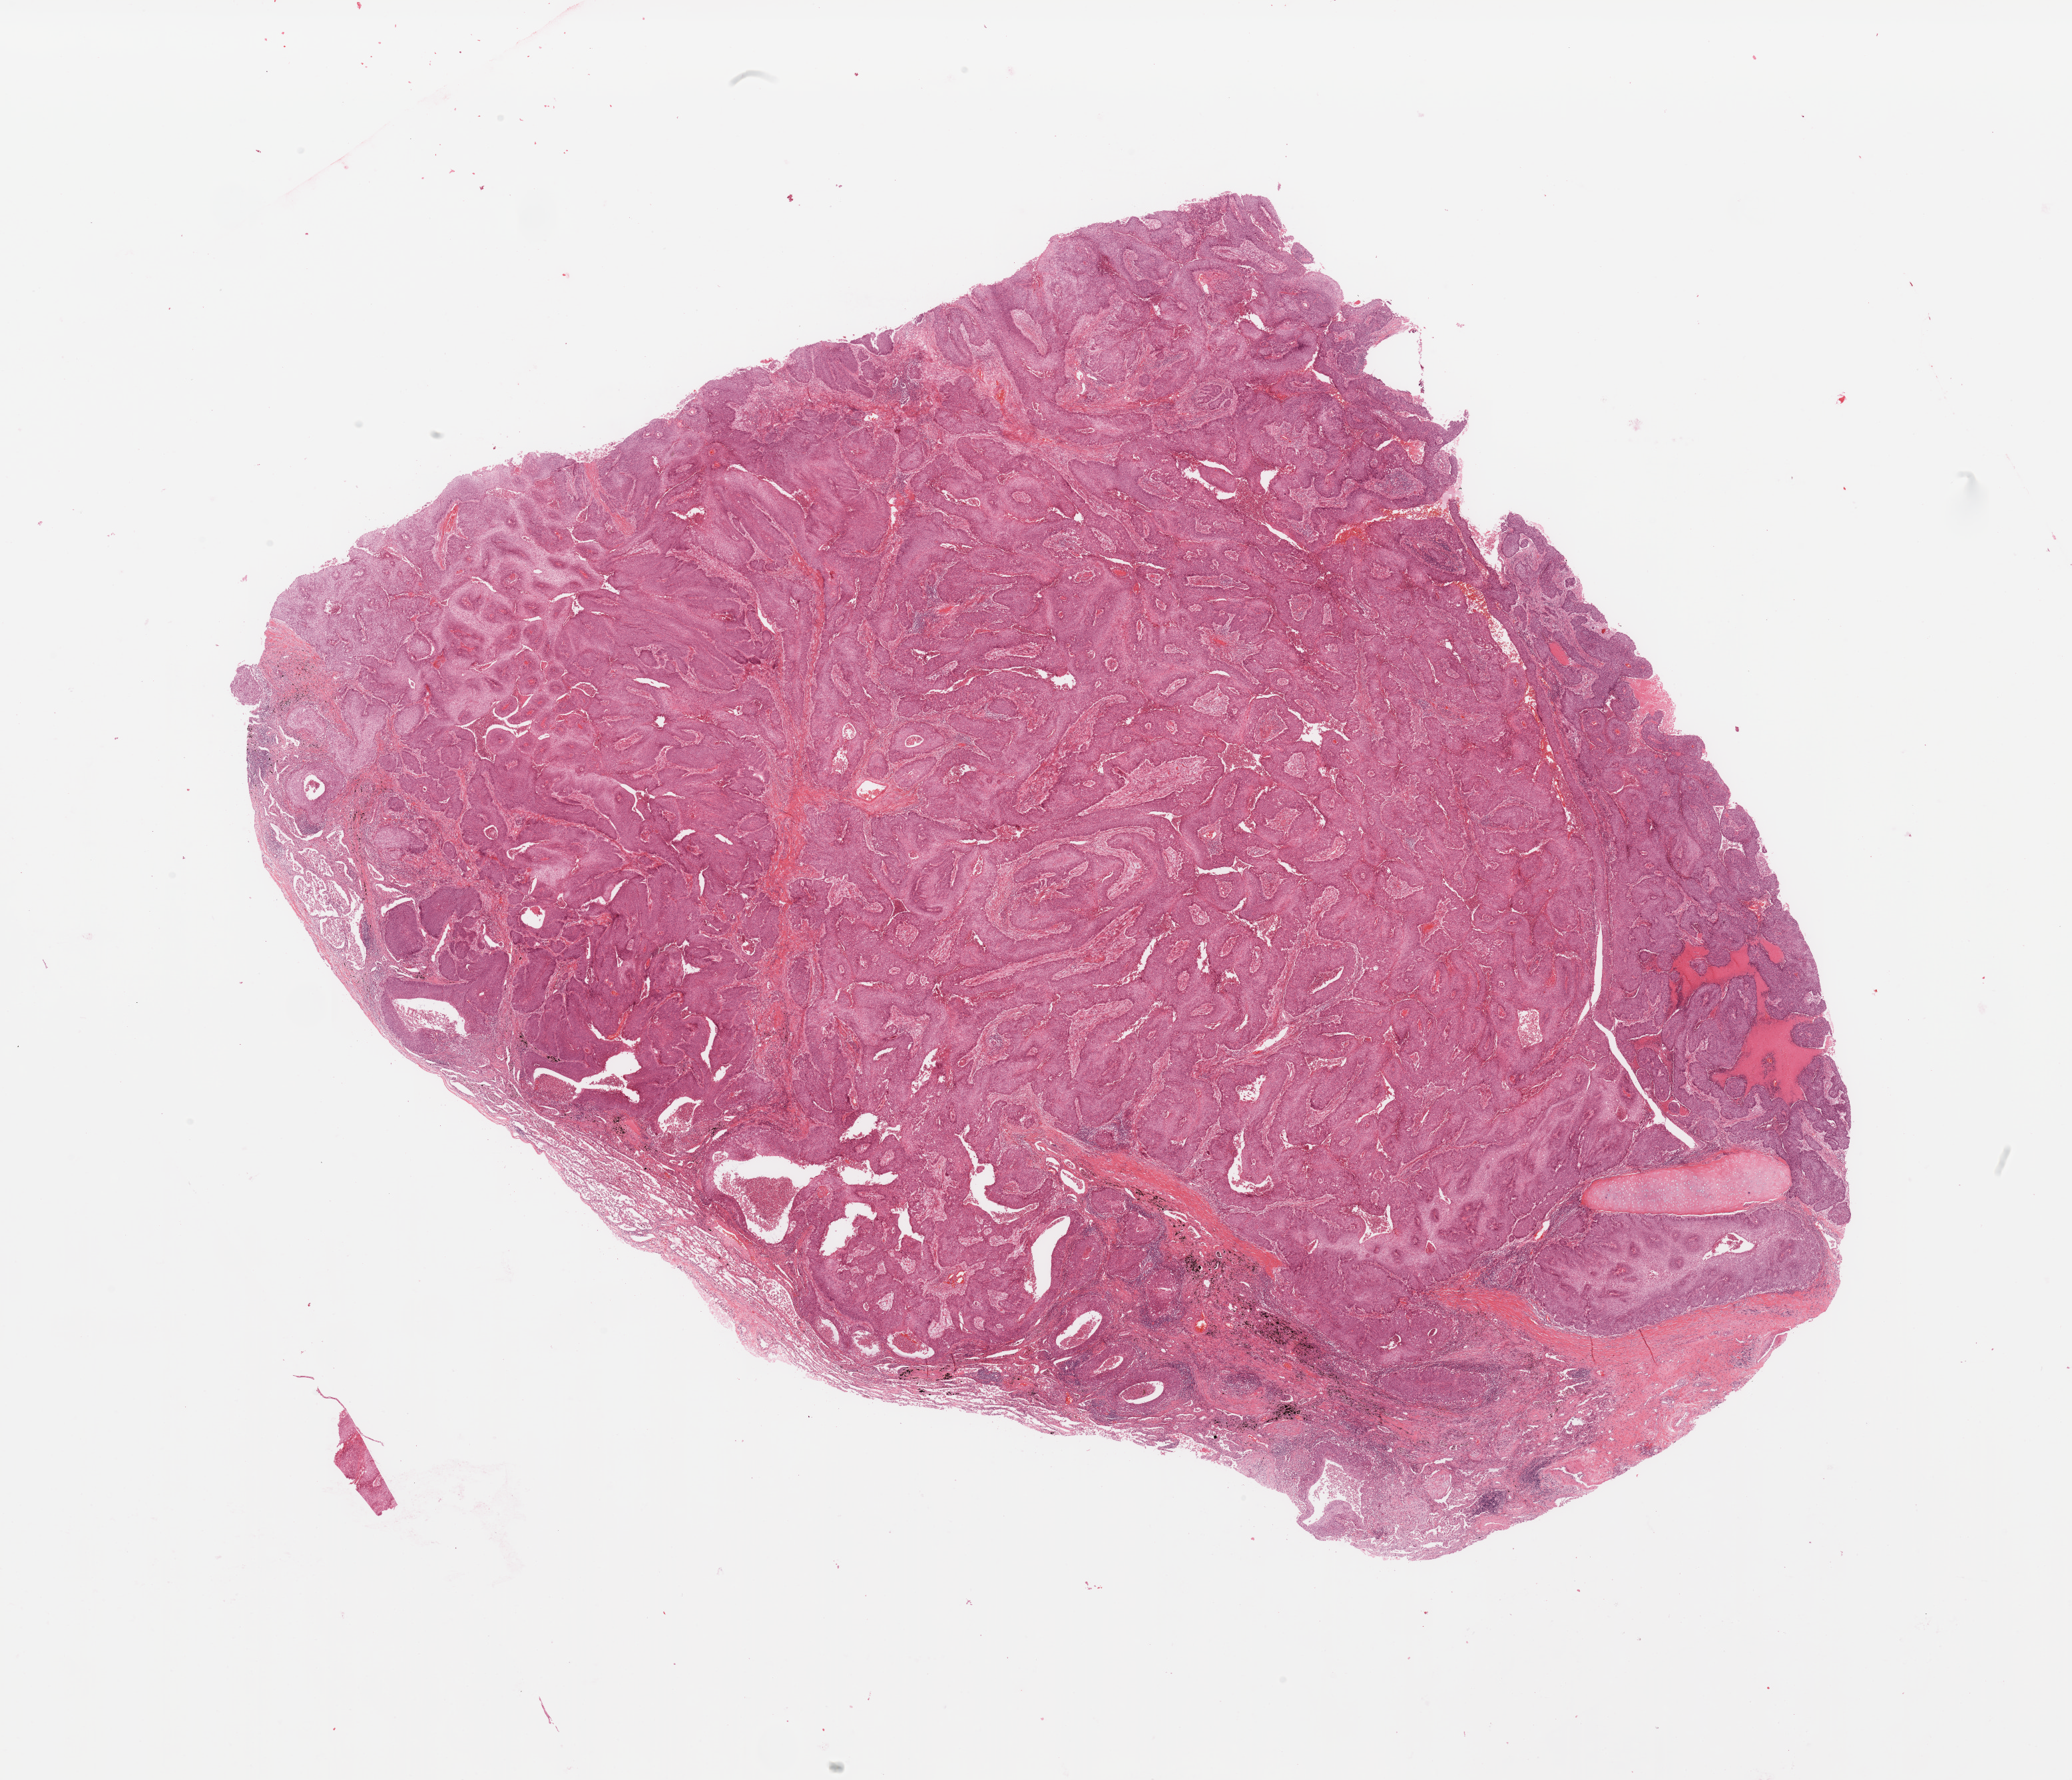
Whole-slide histology image, H&E, a low-resolution overview of the entire scanned area, about 24.6 x 21.1 mm, tumour tissue sample, sampled site: lung. Patient: male, age 64 years.
Histologic diagnosis: Squamous cell carcinoma, NOS.